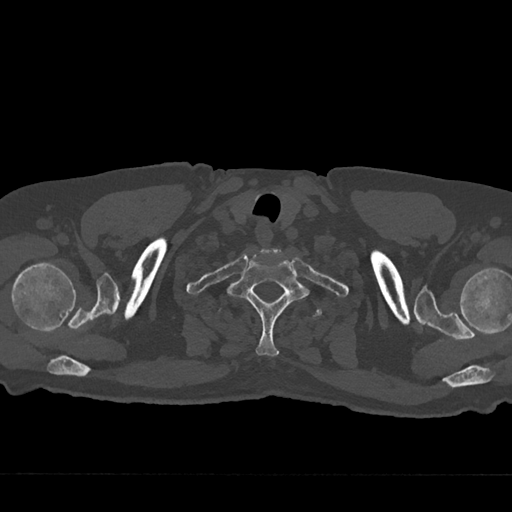
CT including the spine, one axial slice; position 657 of 797 along the scan axis; reconstruction kernel Br40s/3; 120 kVp; bone window (W 1800 / L 400 HU); 0.5 mm slice thickness; 512 × 512 image matrix. Patient: male, 75 years. Case-level facts recorded for this patient, not image findings: primary cancer: renal; vertebrae with lytic lesions (as recorded): T4.
Structures marked on this image (semi-automatically segmented with operator editing):
- T1 vertebra: bounding box (x1, y1, x2, y2) in pixels: (227, 249, 310, 357)
- T2 vertebra: (219, 292, 322, 318)